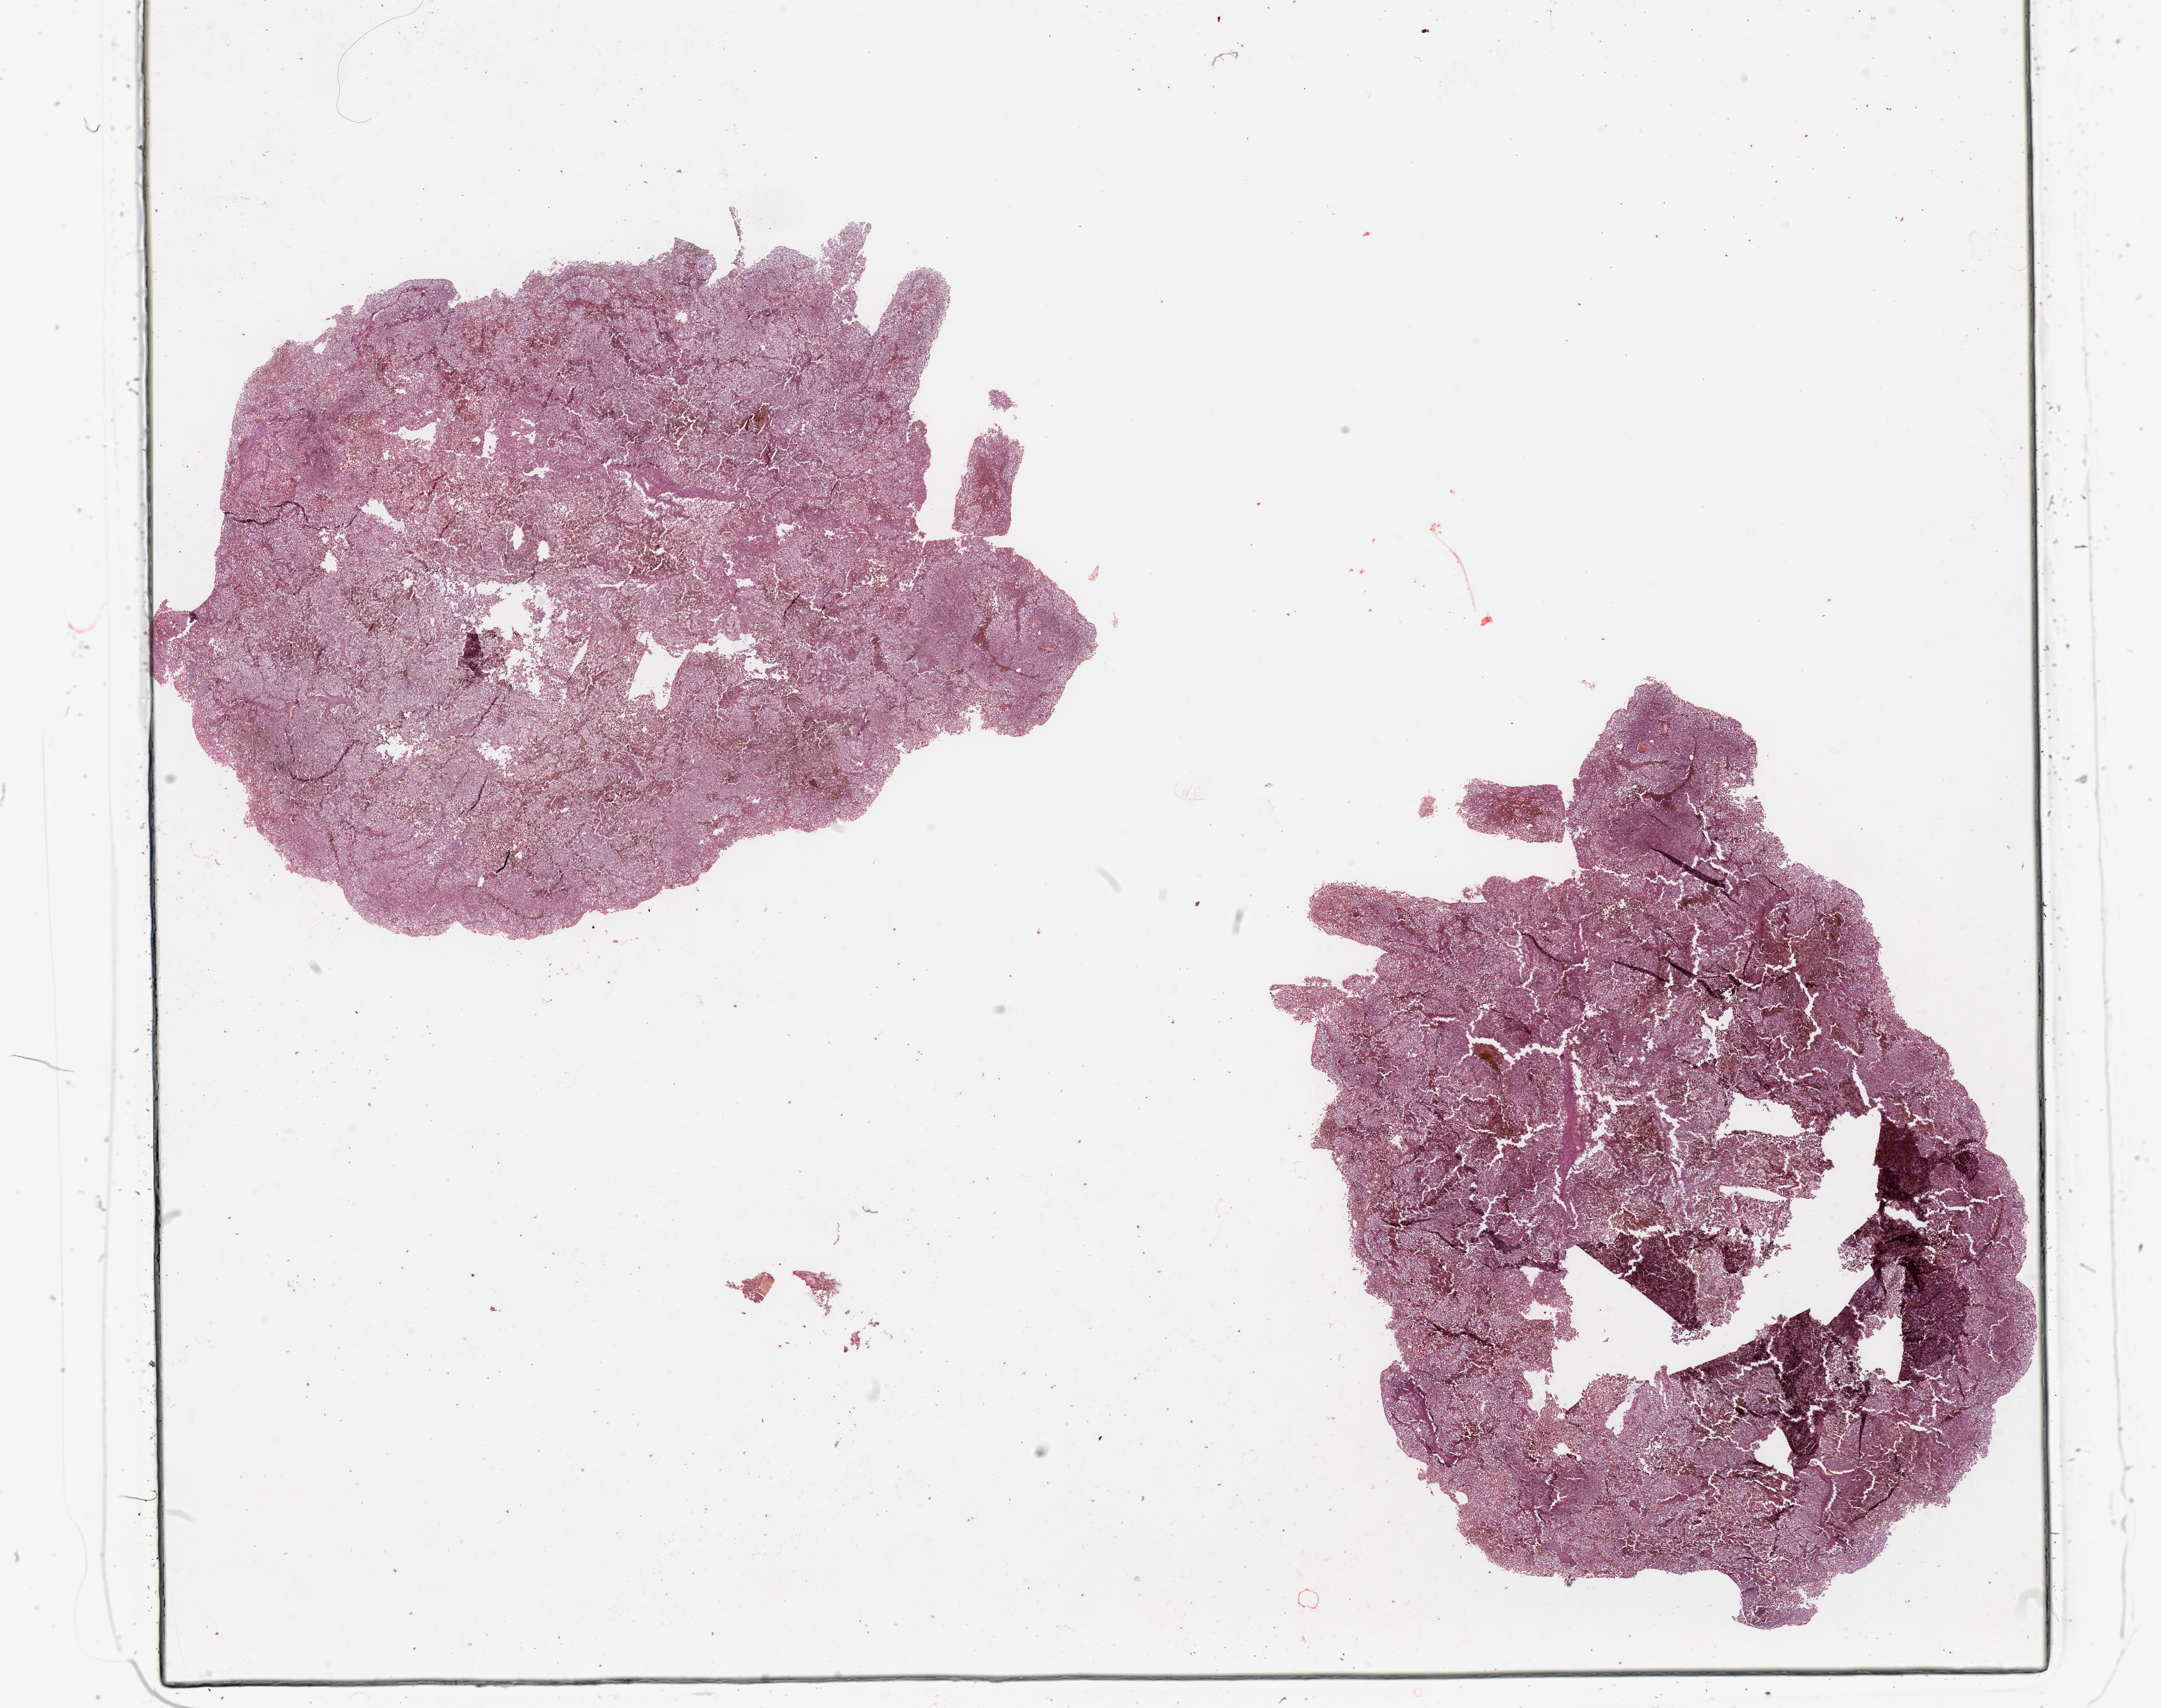
Whole-slide histology image, Hematoxylin and eosin (H&E) stained — whole scanned area (about 27.6 x 21.8 mm) shown as a low-resolution overview; tumour tissue sample, sampled site: skin. Female, 67 y/o. Pathologist review of this section (percent, as recorded): tumour nuclei 95%, necrosis 10%.
This section: metastatic tumour tissue. Patient diagnosis: Malignant melanoma, NOS. Primary tumour site (as recorded): extremities.